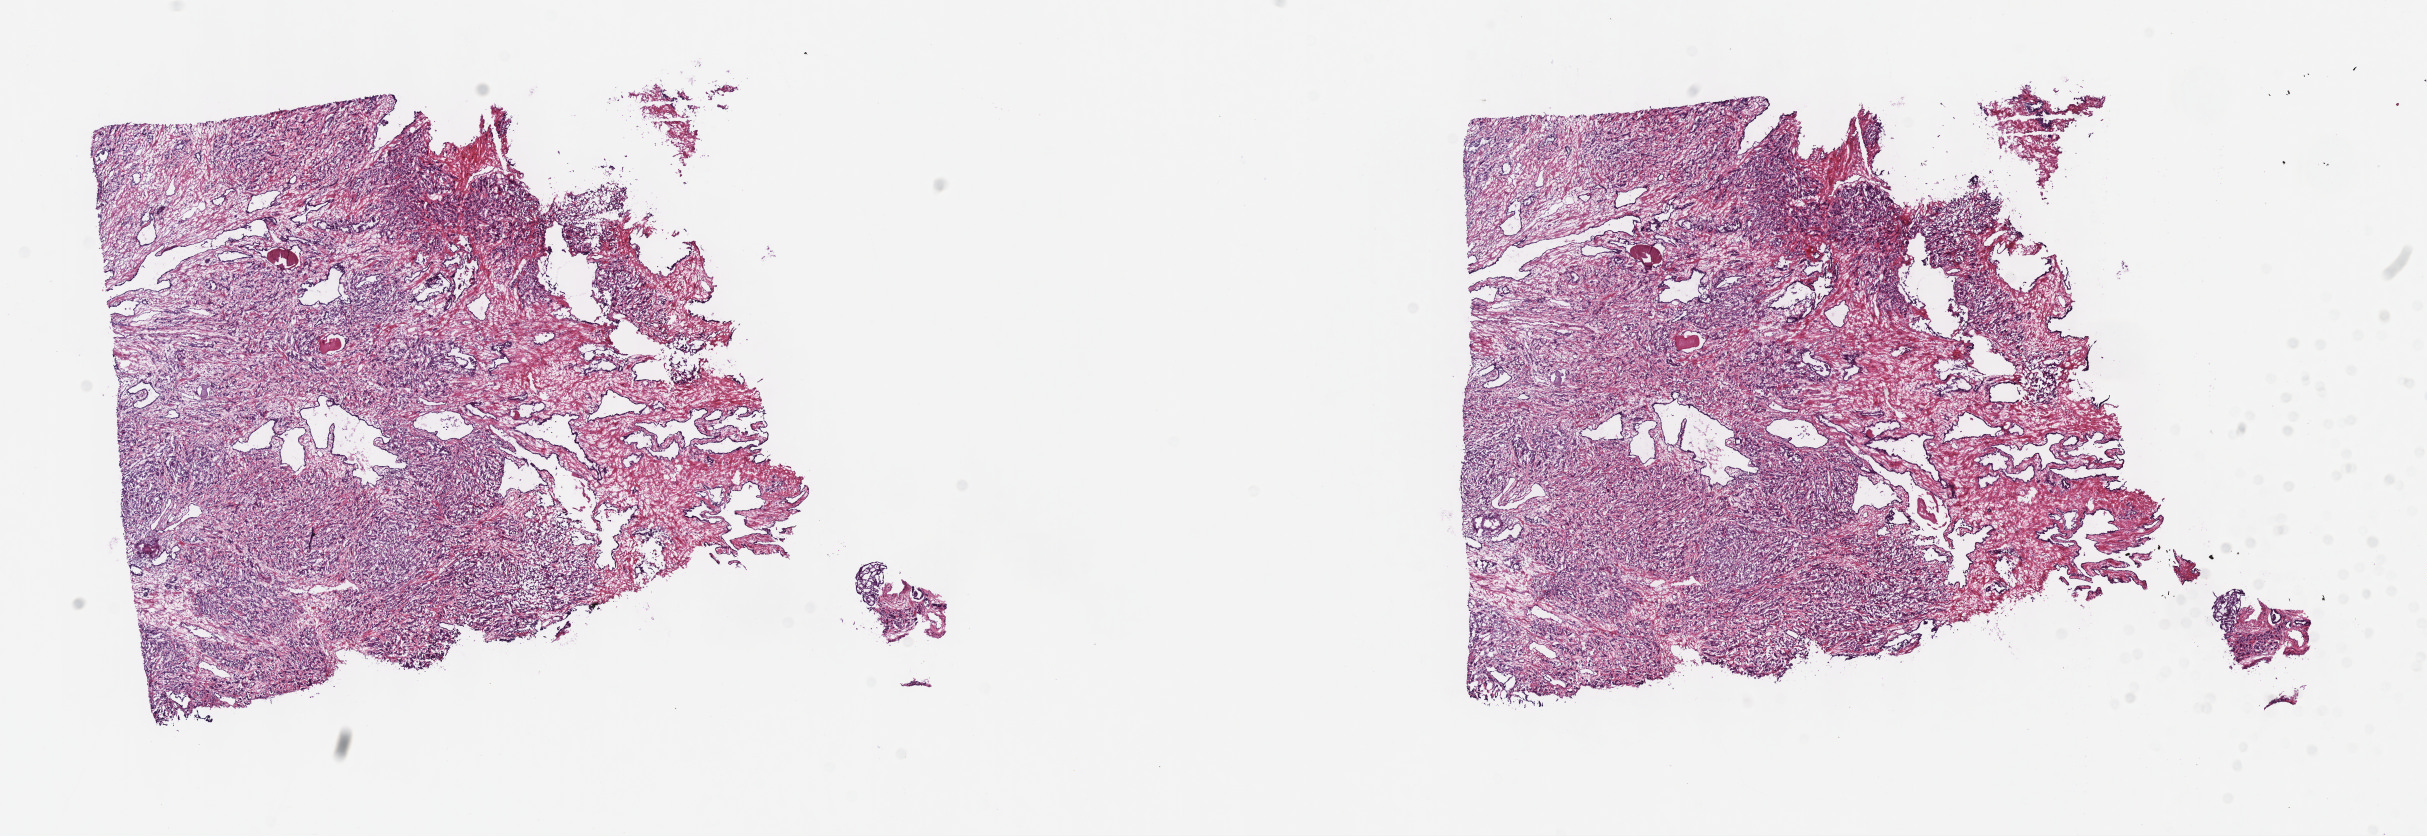
H&E whole-slide image, shown as a low-resolution overview of the whole scanned area (about 19.6 x 6.8 mm, from a 40x scan), frozen section from the top of the tissue portion, sample: primary tumour, prostate. Male, age 58 years at initial diagnosis. Gleason score: 9 (4+5). Pathologist review of this section (percent, as recorded): tumour cells 55%, tumour nuclei 85%, normal cells 10%, stromal cells 35%, necrosis 0%. Infiltration values recorded for this section: lymphocyte infiltration 0%, monocyte infiltration 0%, neutrophil infiltration 0%.
- histologic diagnosis: Adenocarcinoma, NOS (prostate gland)
- laterality: bilateral
- lymph nodes positive (case pathology): 1 of 3 examined